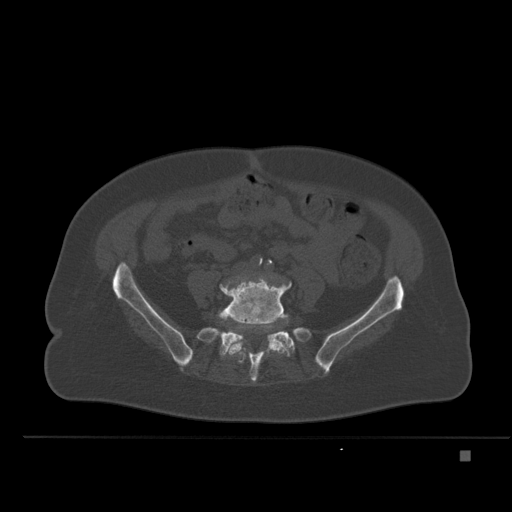
CT including the spine, one axial slice. Slice 157 of 477 in the series (ordered by position). Bone window (W 1800 / L 400 HU). 512 × 512 image matrix, field of view 422 × 422 mm. Patient: female, 74 years. From the clinical record (not read from this slice): primary cancer: colon.
Outlined on this slice (semi-automatic segmentation, software-assisted and operator-edited):
- L5 vertebra: bounding box <219,277,292,357> (left, top, right, bottom; pixels)